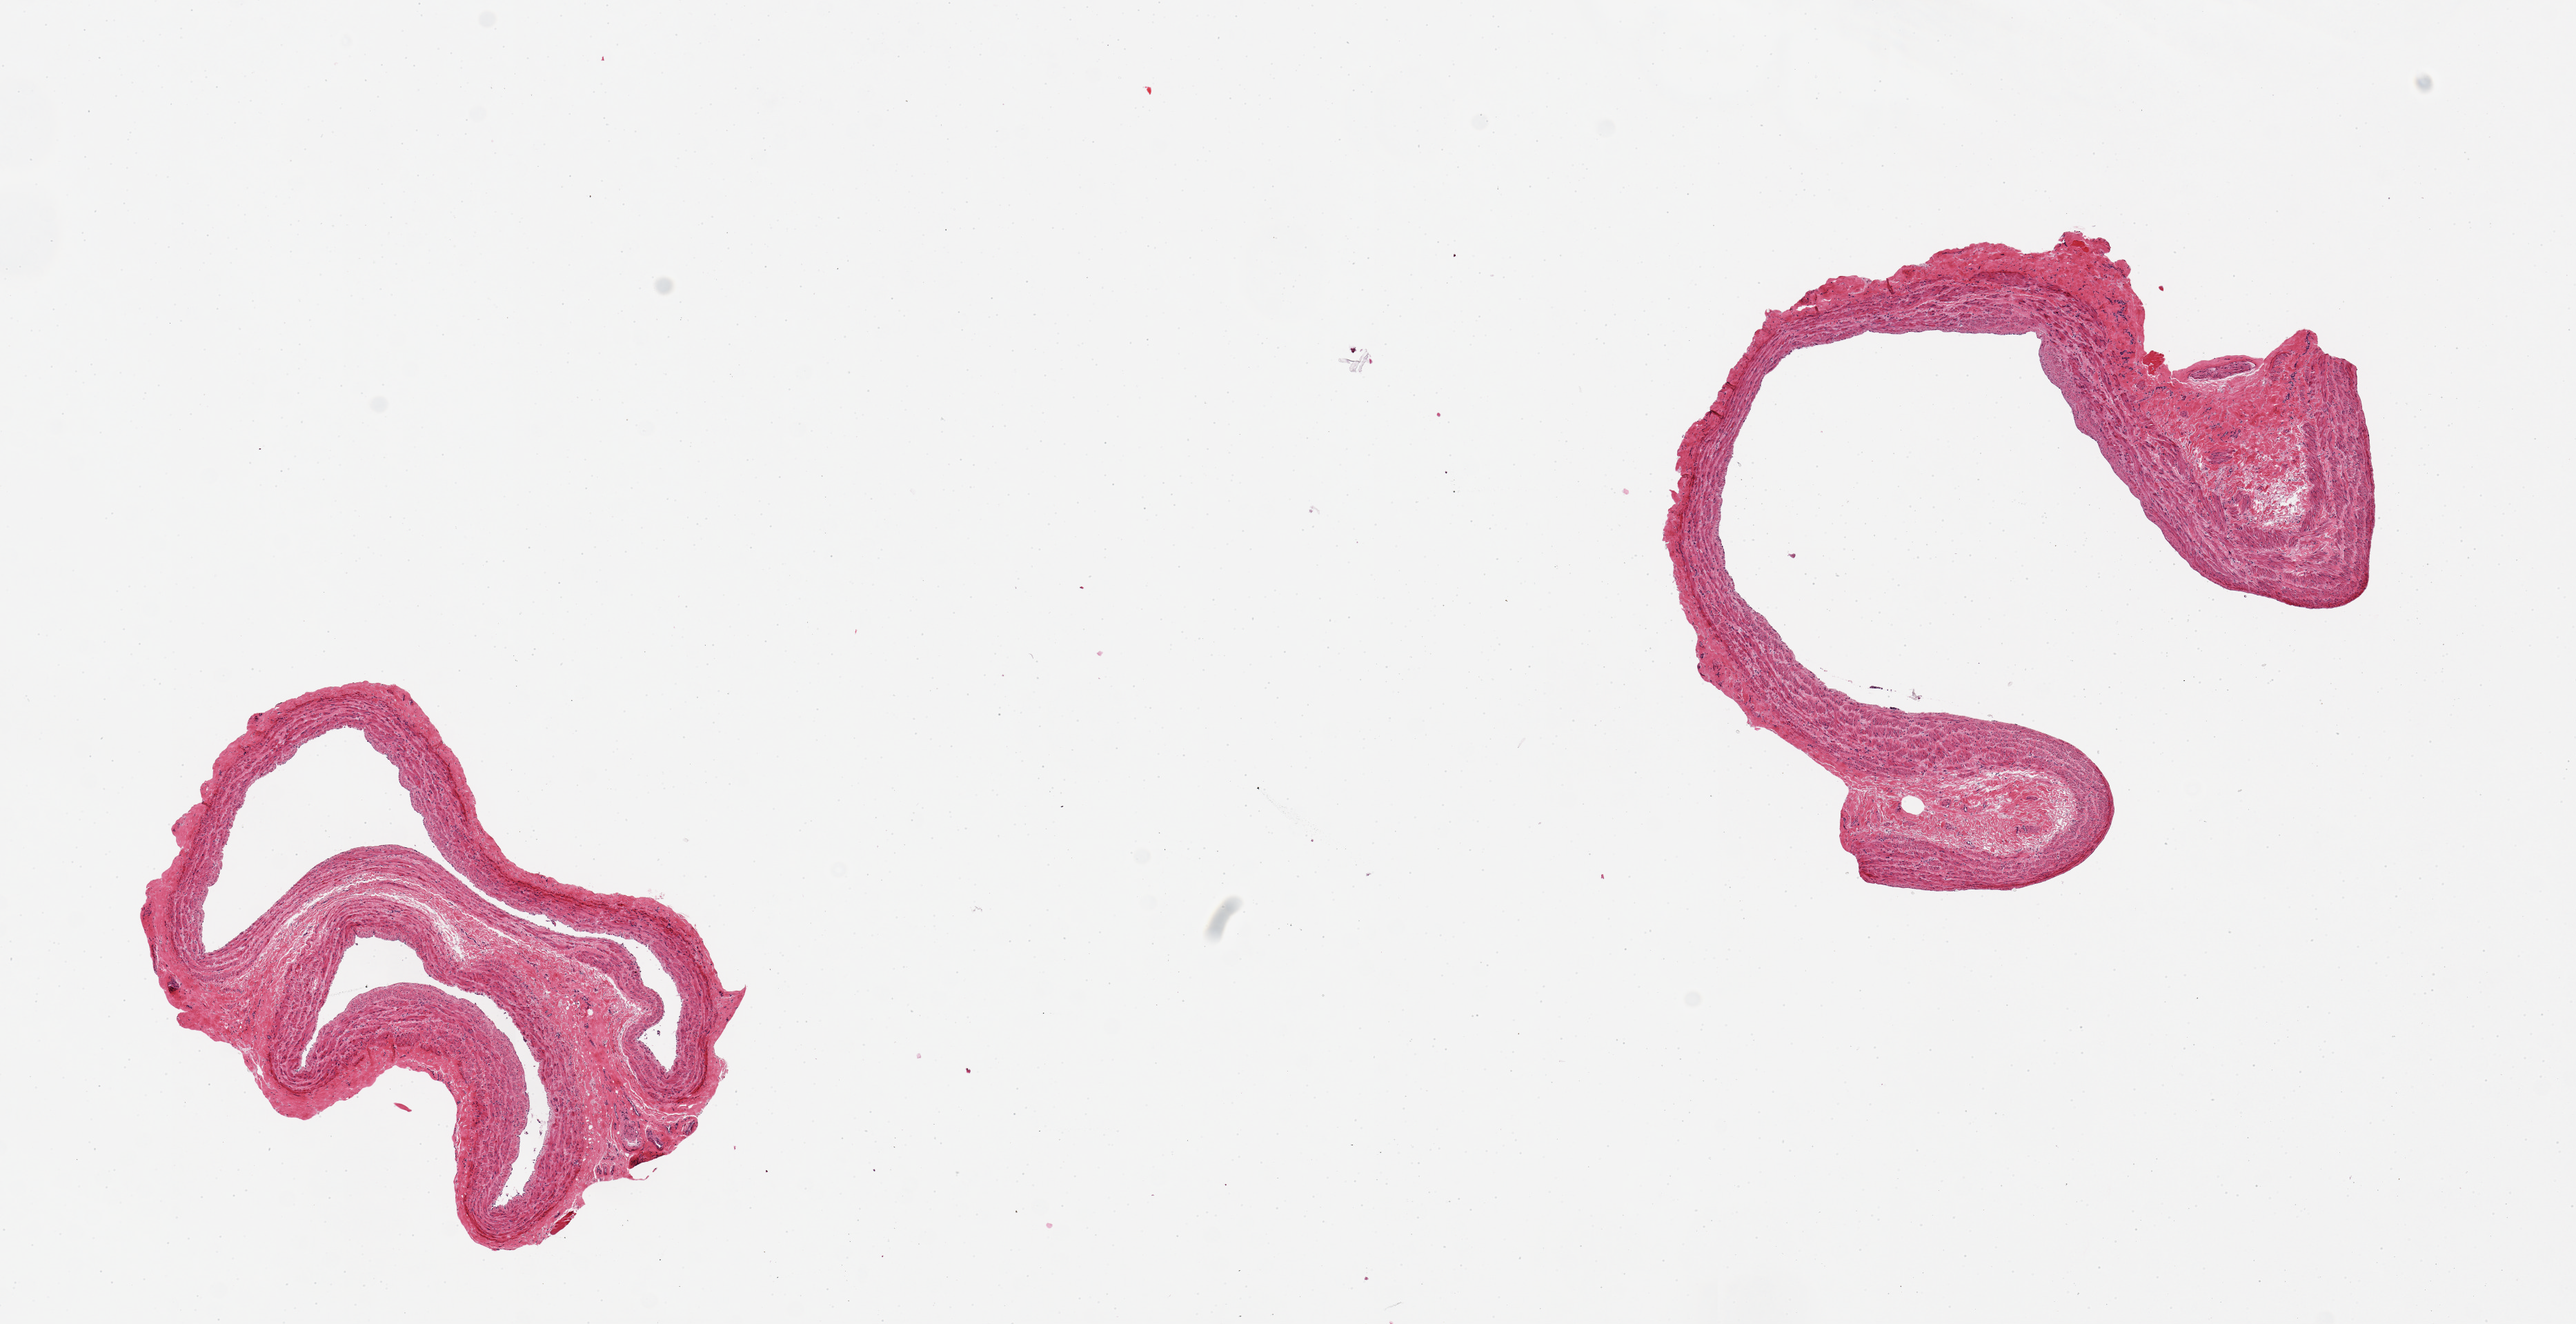
H&E whole-slide image, a low-resolution overview of the entire scanned area, about 14.8 x 7.6 mm (from a 20x scan). PAXgene-fixed paraffin-embedded (PFPE) section. Target tissue: tibial artery. Donor tissue sample.
Reviewer comment on this tissue sample: 2 pieces. 3.5x2 & 4x4mm; Very well trimmed of extraneous tissue.